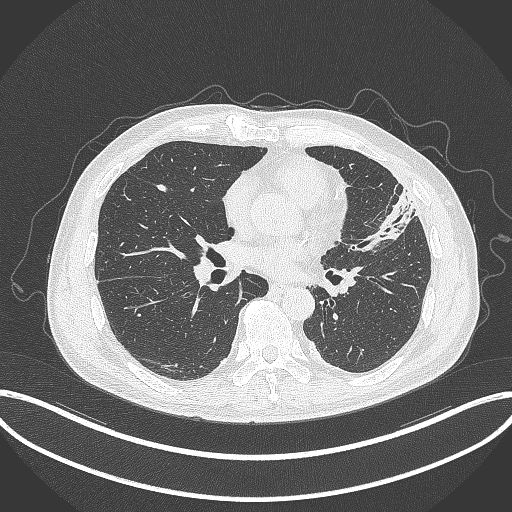
Chest CT, one axial slice; position 156 of 382 along the scan axis; 120 kVp; lung window (W 1500 / L -600 HU); 512 × 512 image matrix, field of view 415 × 415 mm. Male patient, age 64 years. Case-level facts recorded for this patient, not image findings: clinical TNM (as recorded): T4 N1 M0; histopathological grade: G3.
Annotated regions visible in this slice (bounding box drawn by a radiologist):
- lung tumour (recorded histology: adenocarcinoma): bounding box <361,187,419,247> (left, top, right, bottom; pixels)